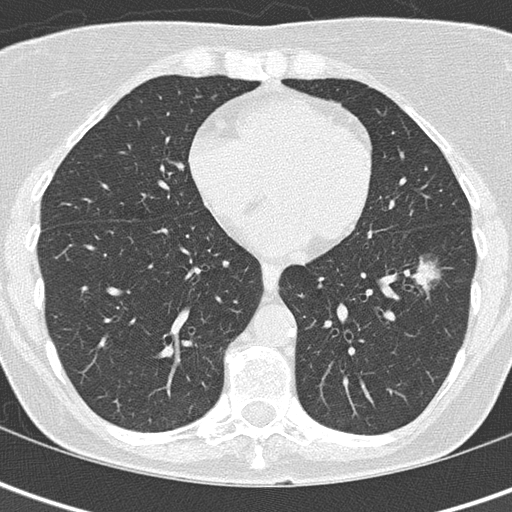
Low-dose screening chest CT, axial slice; baseline screening round; lung window (W 1500 / L -600 HU); 2 mm slice thickness; slice 92 of 149 in the series. Female, age 61 years at enrolment. Former smoker at enrolment.
Expert reader's lesion annotation, bounding box [x1, y1, x2, y2] px = [379, 248, 453, 304]. Screening reader's record for this exam (one nodule recorded; not confirmed to be the boxed lesion): non-calcified nodule or mass ≥4 mm, left lower lobe, 29 × 16 mm, ground glass attenuation. Official screen result: positive, change unspecified: nodule(s) >= 4 mm or enlarging nodule(s), mass(es), or other non-specific abnormalities suspicious for lung cancer. Later outcome: lung cancer diagnosed 259 days after this screen — bronchiolo-alveolar adenocarcinoma, NOS, left lower lobe, well differentiated (G1), stage IA (AJCC 6th edition), 10 mm at pathology.